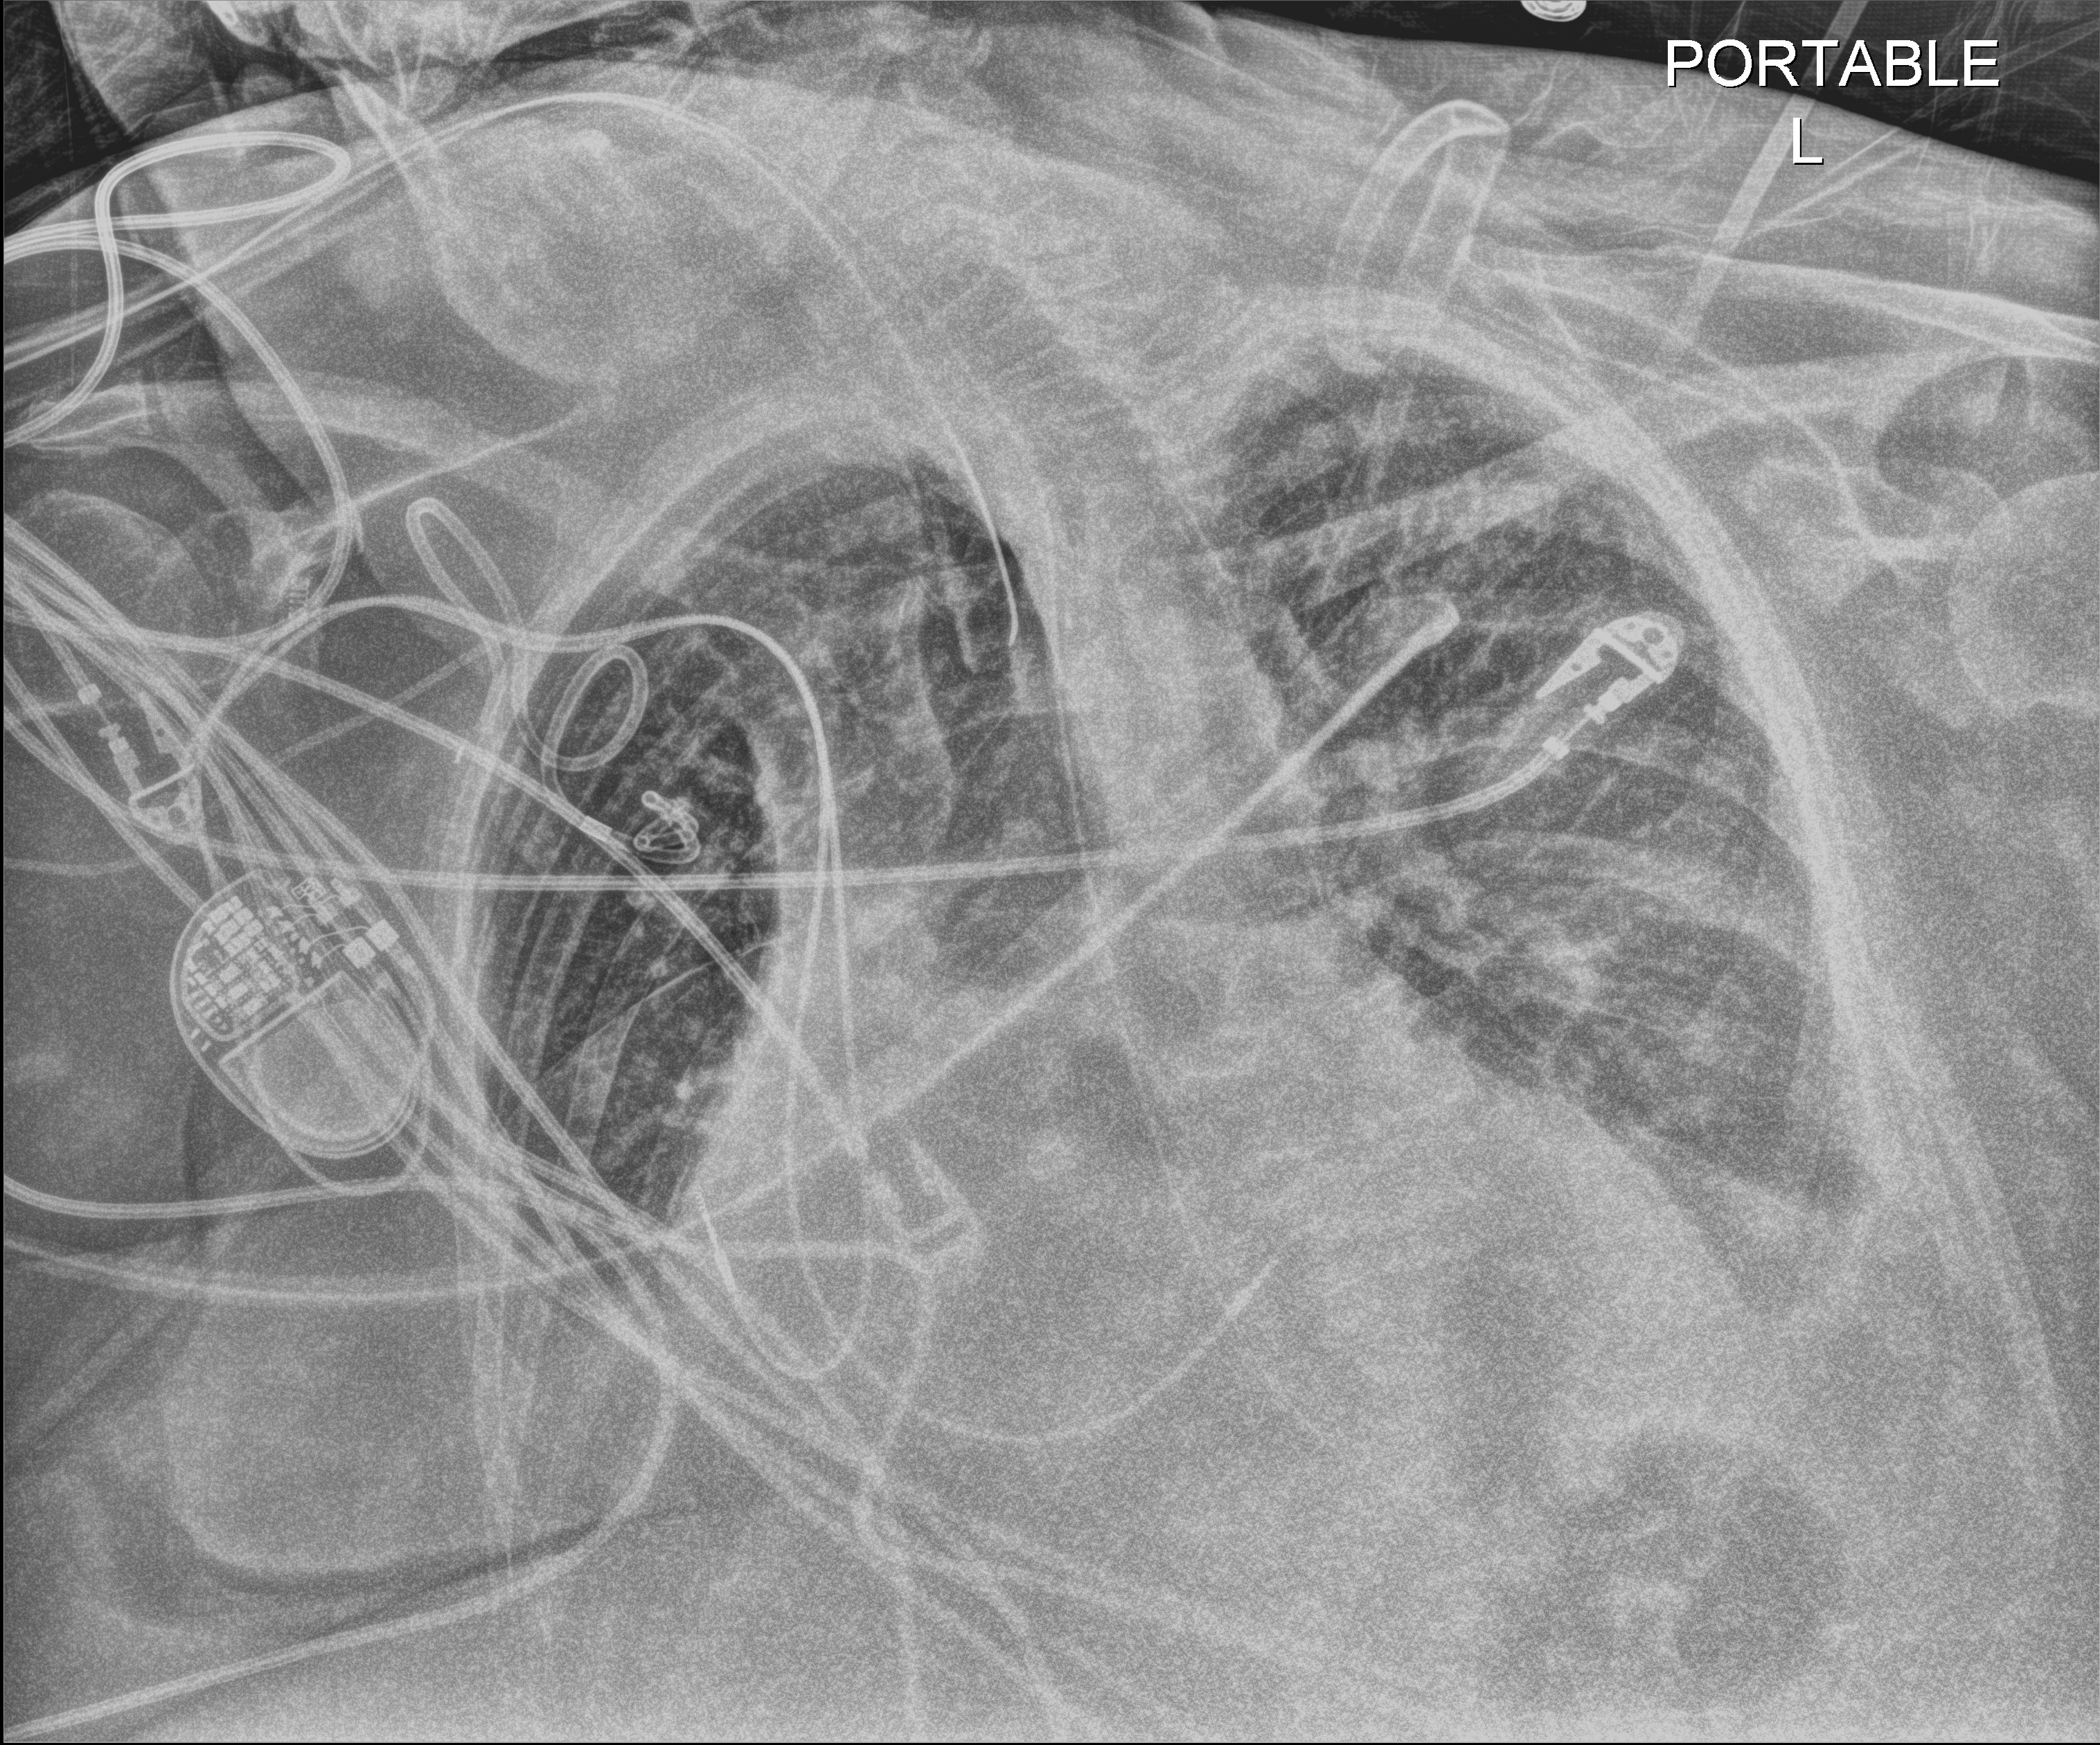
Portable chest radiograph, anteroposterior (AP) projection. Patient hospitalised with COVID-19; female, aged 75–90 years.
Hospital-stay facts (about this admission, not read from this image; timing relative to this image not recorded): admitted to intensive care during this hospital stay: yes; length of hospital stay: 21 days.